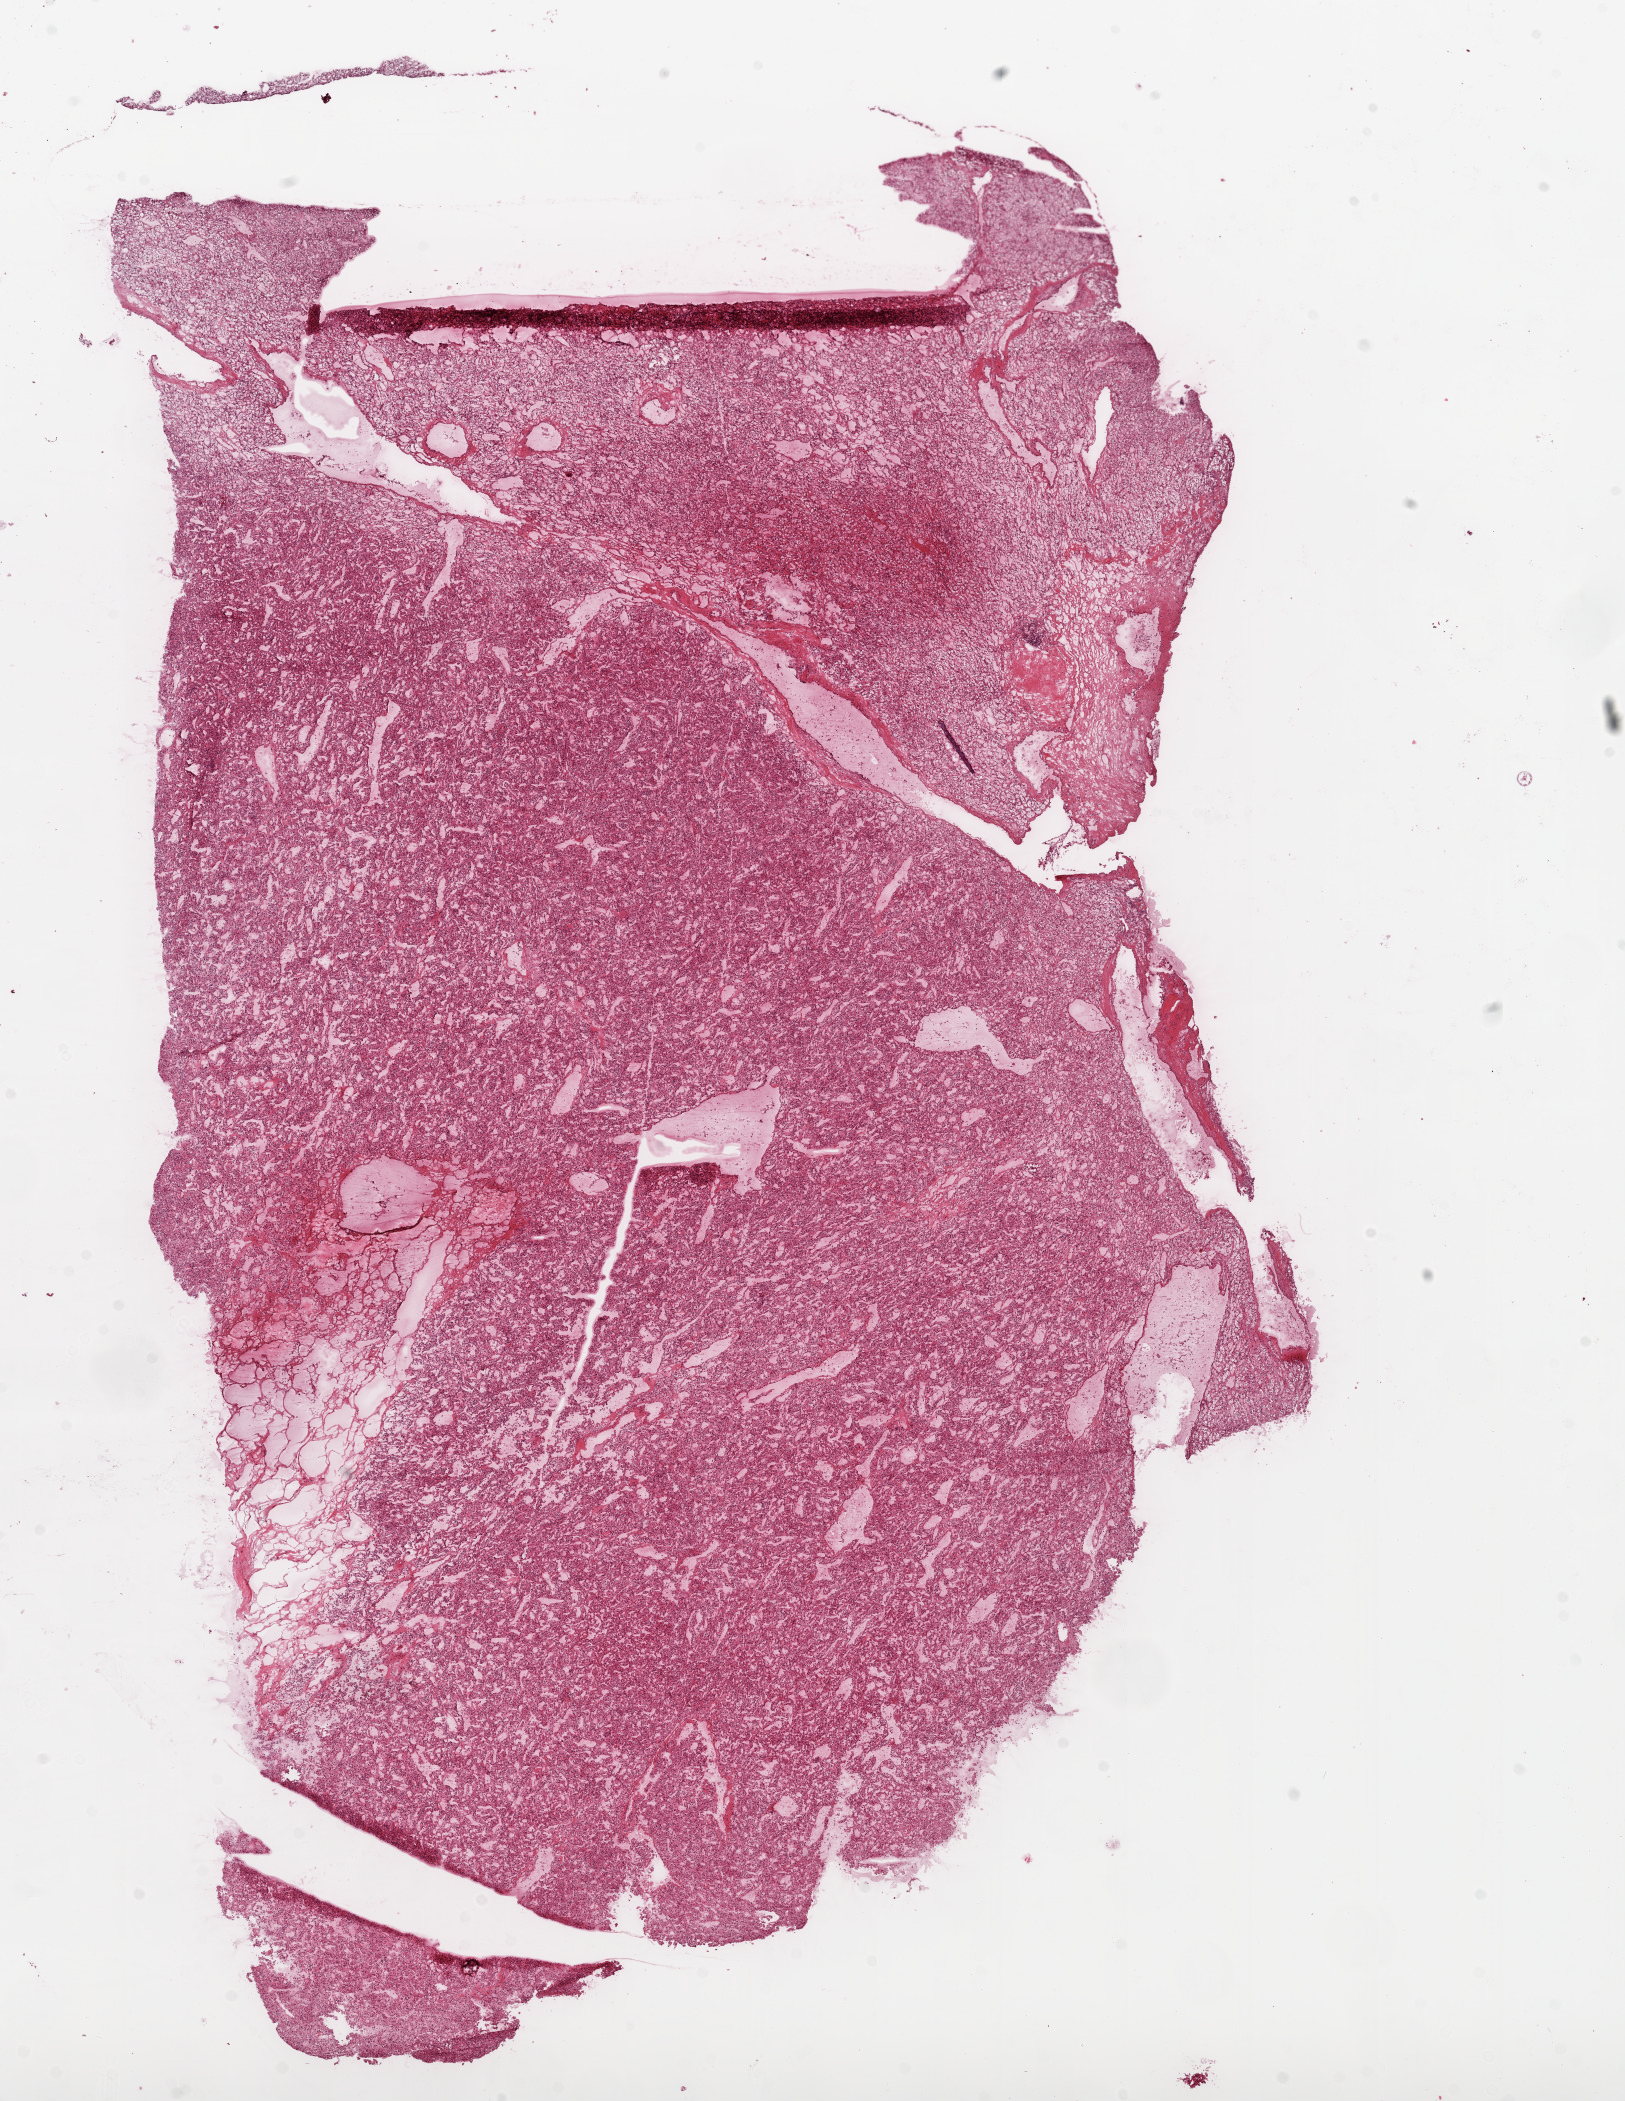
Digitized Hematoxylin and eosin (H&E) stained tissue section (whole slide) — whole scanned area (about 13.0 x 16.9 mm) shown as a low-resolution overview. Frozen section from the top of the tissue portion. Primary tumour sample from the kidney. Female, age 43 years at initial diagnosis. Histologic grade: G2 (moderately differentiated). Pathologist review of this section (percent, as recorded): tumour cells 90%, tumour nuclei 85%, normal cells 0%, stromal cells 10%, necrosis 0%.
Pathologic diagnosis: Clear cell adenocarcinoma, NOS. Laterality: right. AJCC pathologic stage: I.